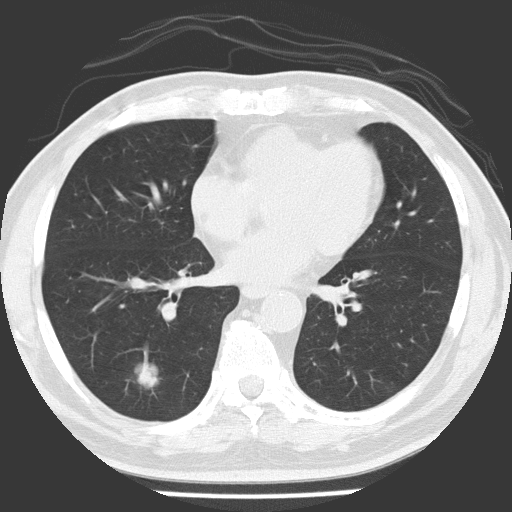
Low-dose screening chest CT, one axial slice. Position 68 of 154 along the scan axis. 120 kVp. Lung window (W 1500 / L -600 HU). 2 mm slice thickness. 512 × 512 image matrix, field of view 311 × 311 mm.
Structures marked on this image (outlined manually by an expert reader):
- lesion 1 (tumor, lower lobe of right lung): bounding box (x1, y1, x2, y2) in pixels: (136, 362, 158, 387)